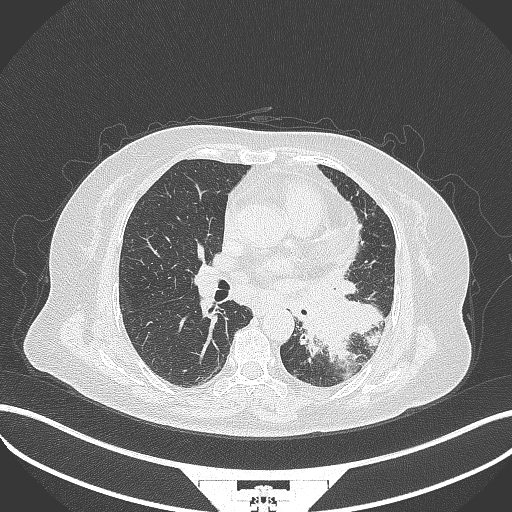
Chest CT, one axial slice. Position 178 of 322 along the scan axis. 120 kVp. Lung window (W 1500 / L -600 HU). 1 mm slice thickness. 512 × 512 image matrix, field of view 400 × 400 mm. Female patient, age 69 years. From the clinical record (not read from this slice): clinical TNM (as recorded): T2b N3 M1.
Annotated regions visible in this slice (rectangle marked by the reading radiologist):
- lung tumour (recorded histology: adenocarcinoma): box from (x=299, y=288) to (x=383, y=364) px